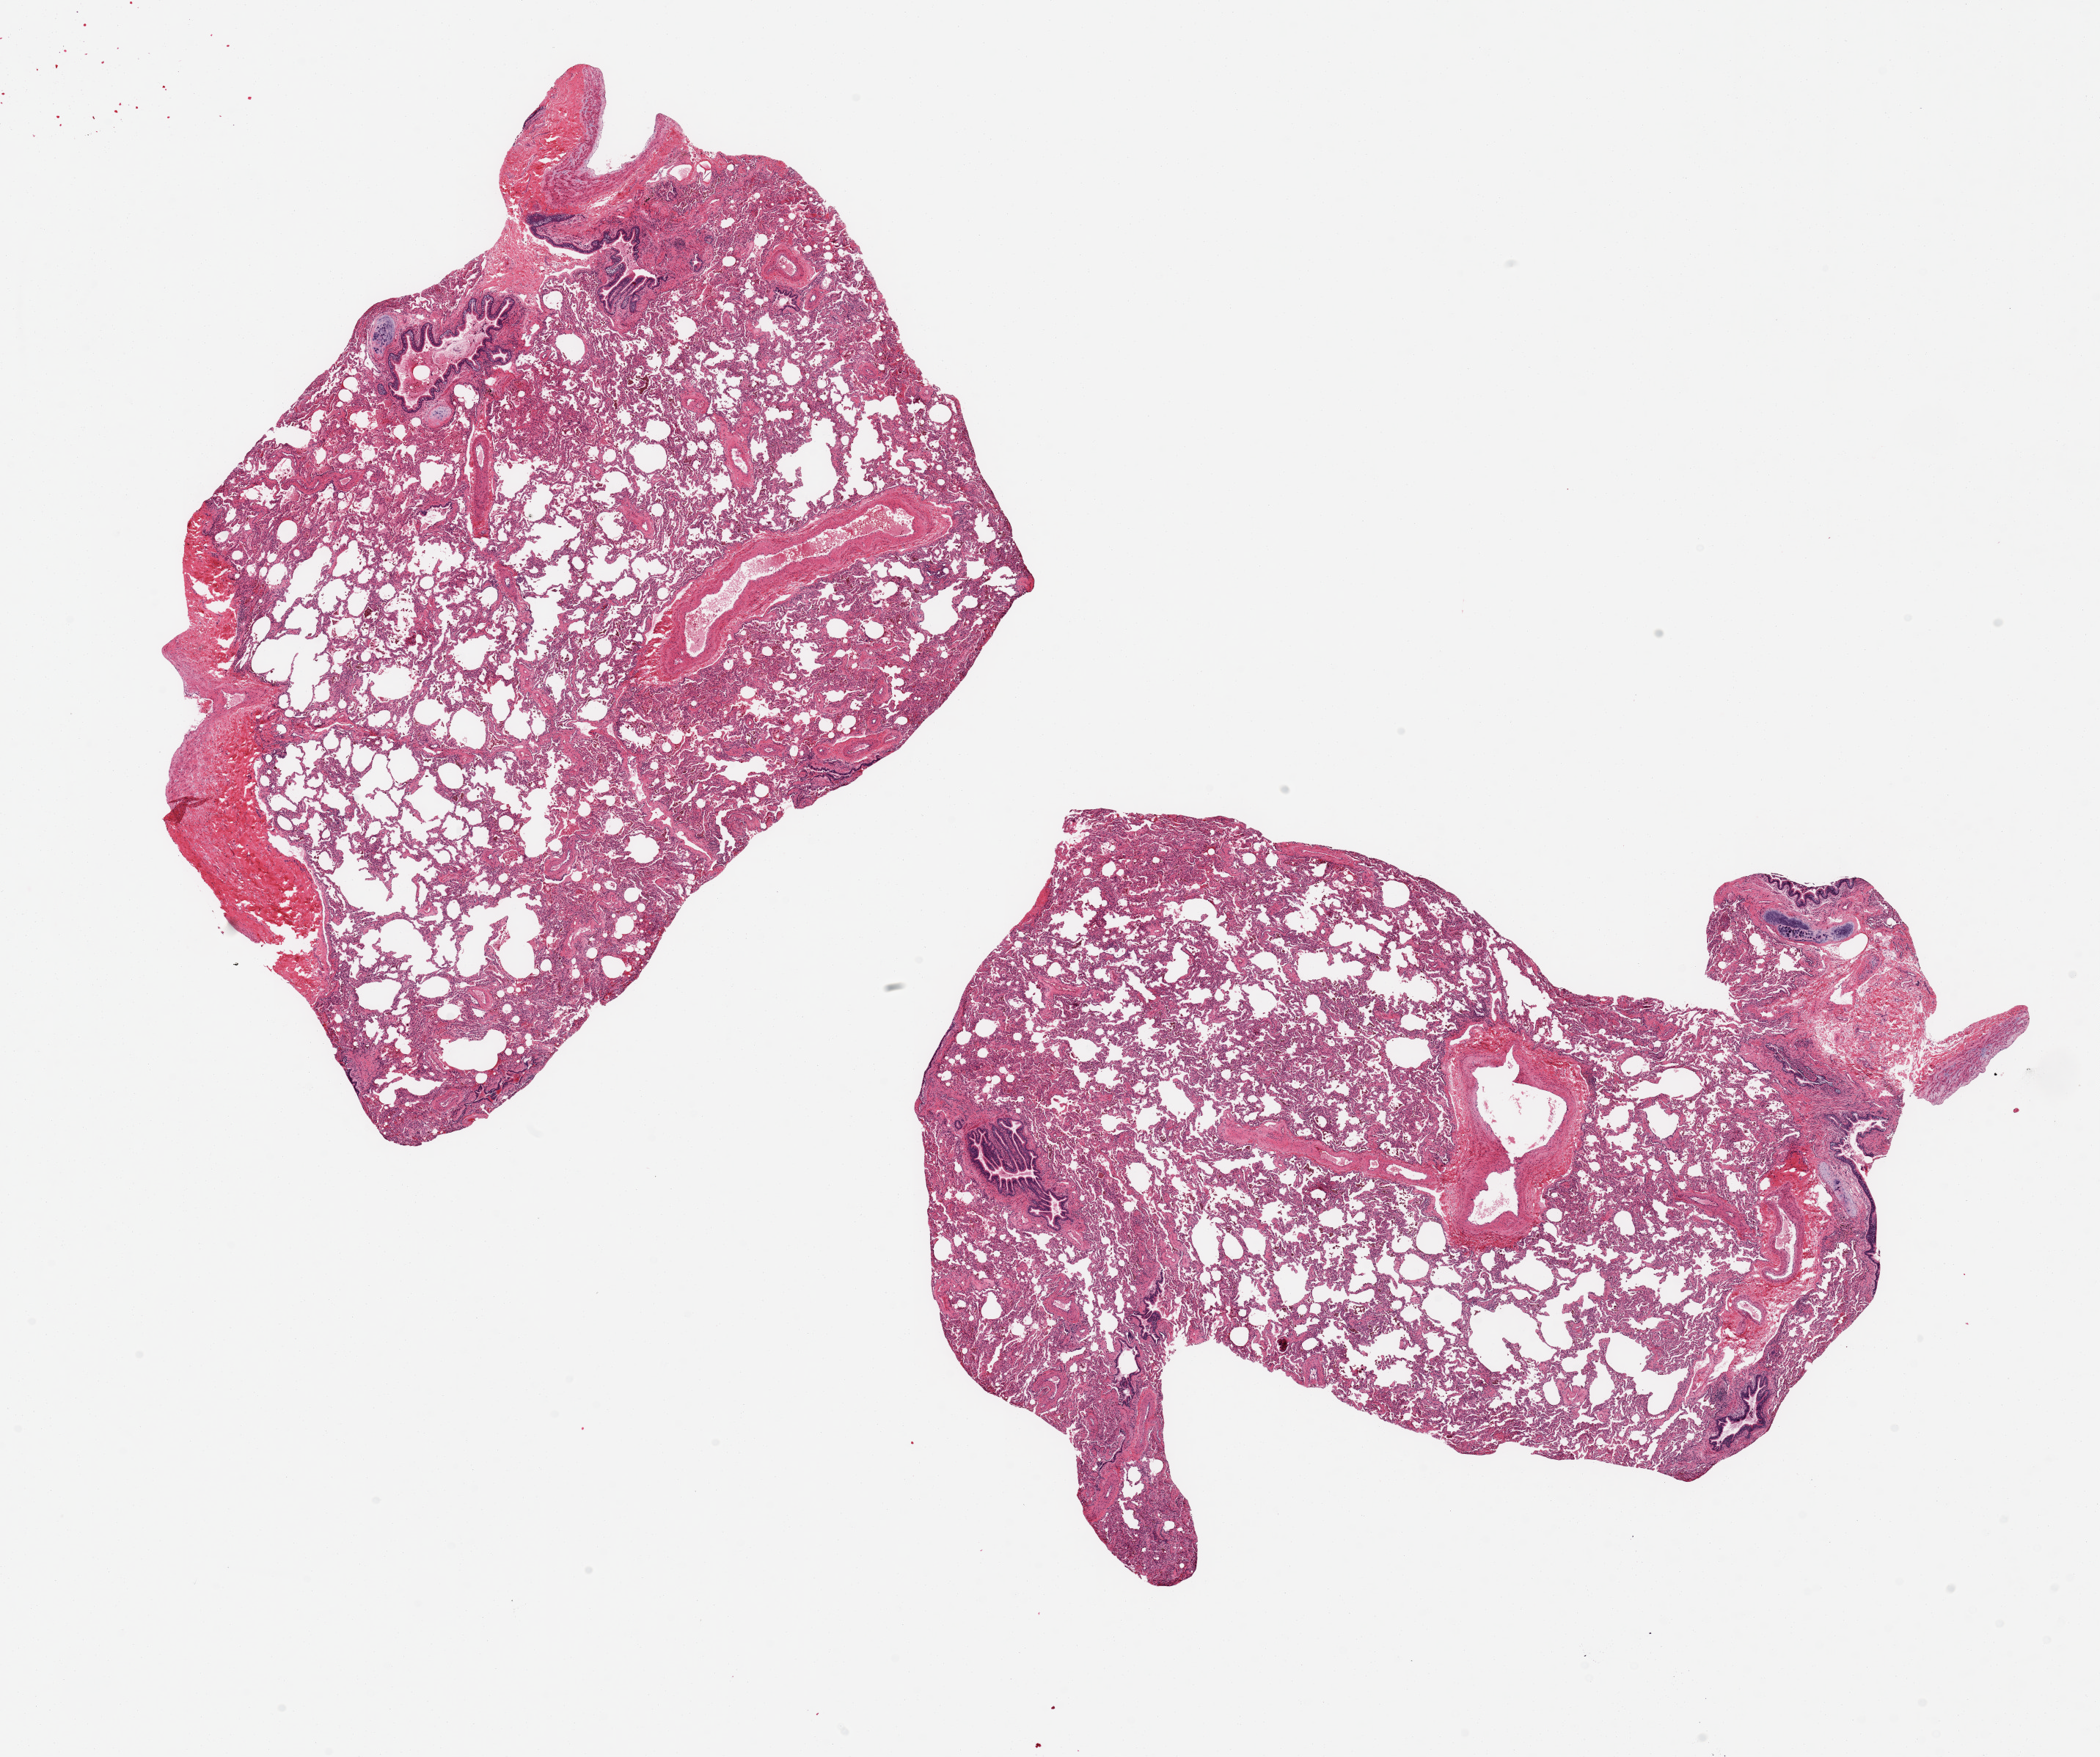
Haematoxylin and eosin whole-slide image, brightfield — a low-resolution overview of the entire scanned area, about 22.6 x 18.9 mm, PAXgene-fixed paraffin-embedded (PFPE) section, sampled site (target tissue): lung, tissue donor sample. Female donor.
Reviewer comment on this tissue sample: 2 aliquots, ~ 9x6mm. Mild congestion; prominent mucoid secretions in bronchus.